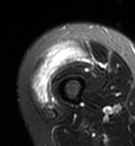
MRI of an extremity soft-tissue mass, one axial slice. Slice 16 of 95 in the series (ordered by position). T2-weighted fat-saturated. MR volume resampled by the dataset authors to the PET/CT grid (not the native acquisition matrix). 3.27 mm slice thickness. 135 × 146 image matrix, field of view 132 × 143 mm. Female patient. Case-level facts recorded for this patient, not image findings: histological type: pleiomorphic undifferentiated sarcoma; grade: high; site of the primary tumour: right quadricep.
Structures marked on this image (expert contour drawn on MRI and transferred to this co-registered scan by the dataset authors):
- gross tumour volume including surrounding oedema: bounding box [x1, y1, x2, y2] px = [32, 41, 86, 105]